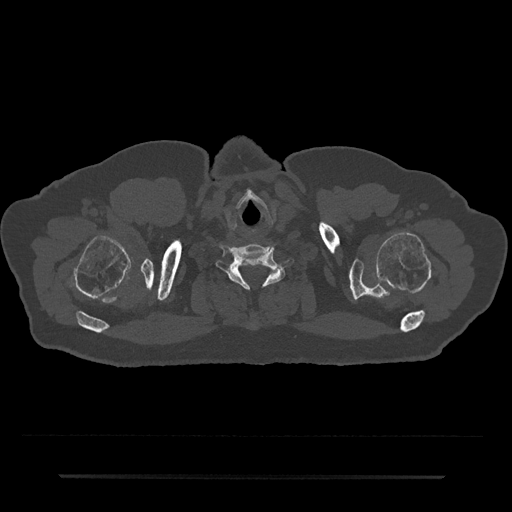
CT including the spine, one axial slice. Position 668 of 797 along the scan axis. 120 kVp. Bone window (W 1800 / L 400 HU). 0.5 mm slice thickness. 512 × 512 image matrix, field of view 437 × 437 mm. Male patient, age 69 years. From the clinical record (not read from this slice): primary cancer: prostate.
Structures marked on this image (semi-automatically segmented with operator editing):
- T1 vertebra: bounding box (x1, y1, x2, y2) in pixels: (269, 271, 278, 277)